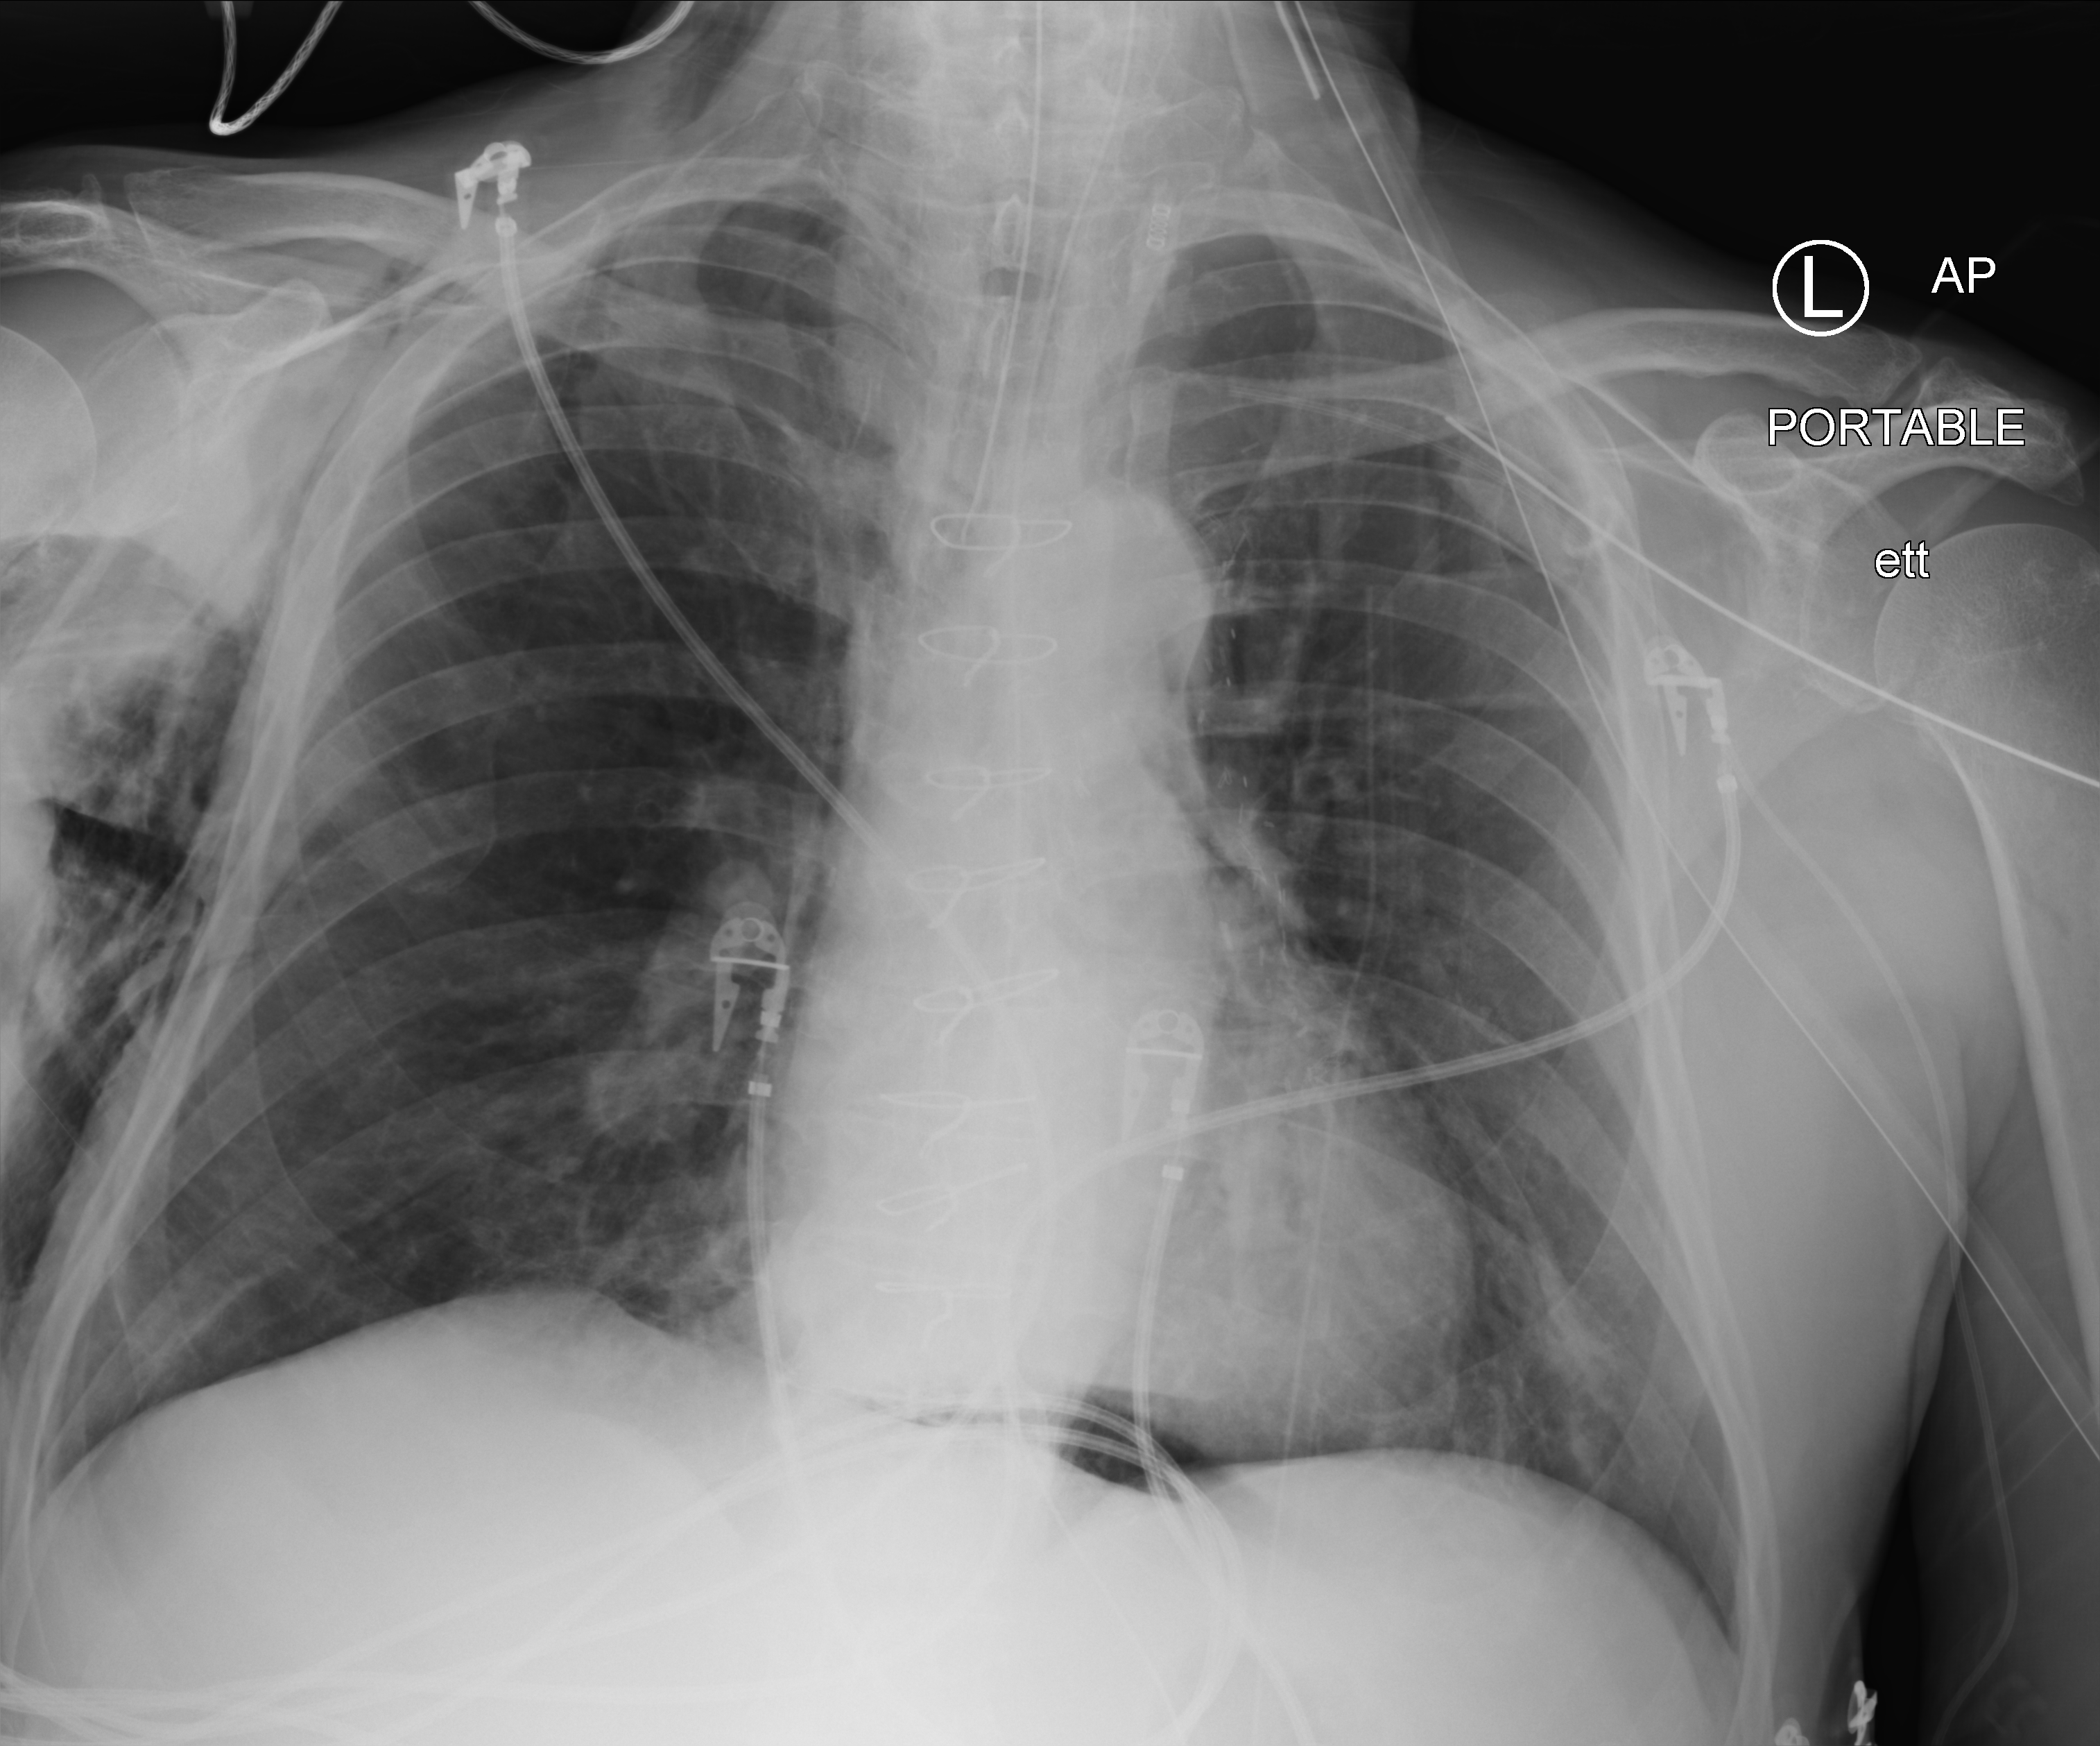
Bedside chest radiograph (computed radiography); anteroposterior (AP) projection. Patient hospitalised with COVID-19; male, aged 60–74 years.
Hospital-stay facts (about this admission, not read from this image; timing relative to this image not recorded): COPD (admission record): no; mechanically ventilated during this hospital stay: yes; length of hospital stay: 22 days.